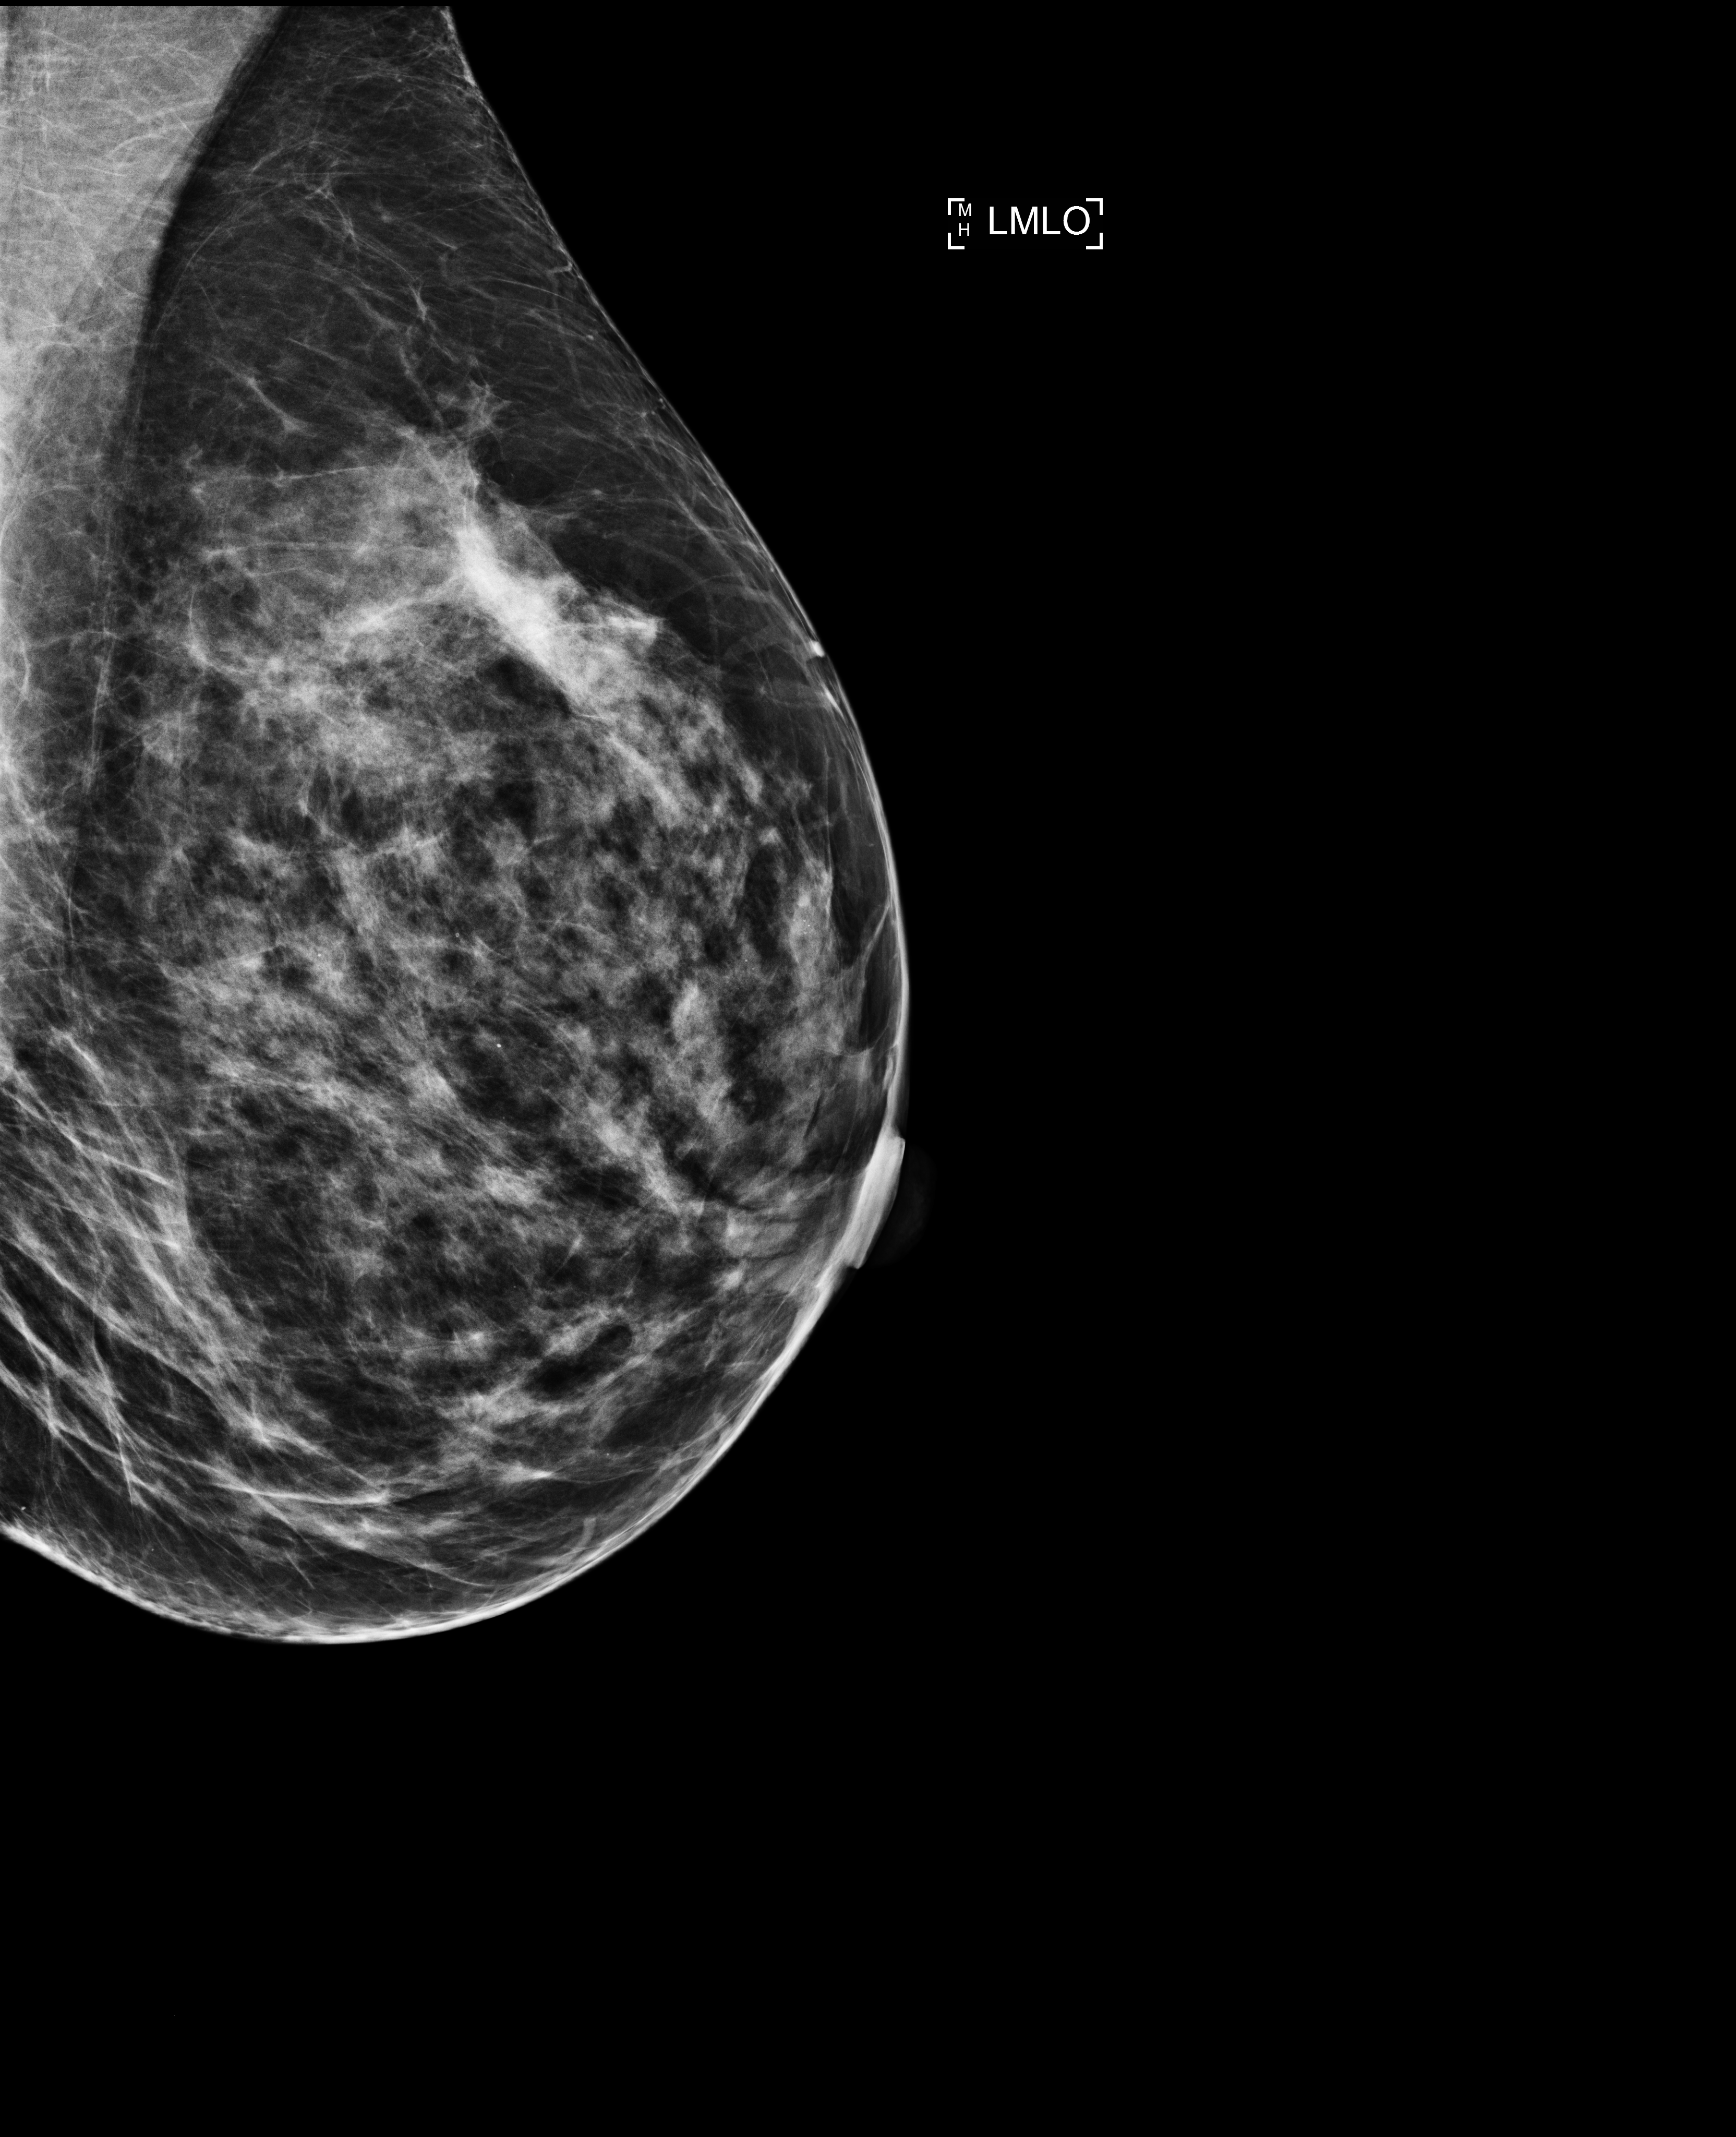
Screening examination; system: Selenia Dimensions. Patient: female, 48 years.
Image type: full-field digital mammogram. Breast: left. Projection: mediolateral oblique (MLO) view.